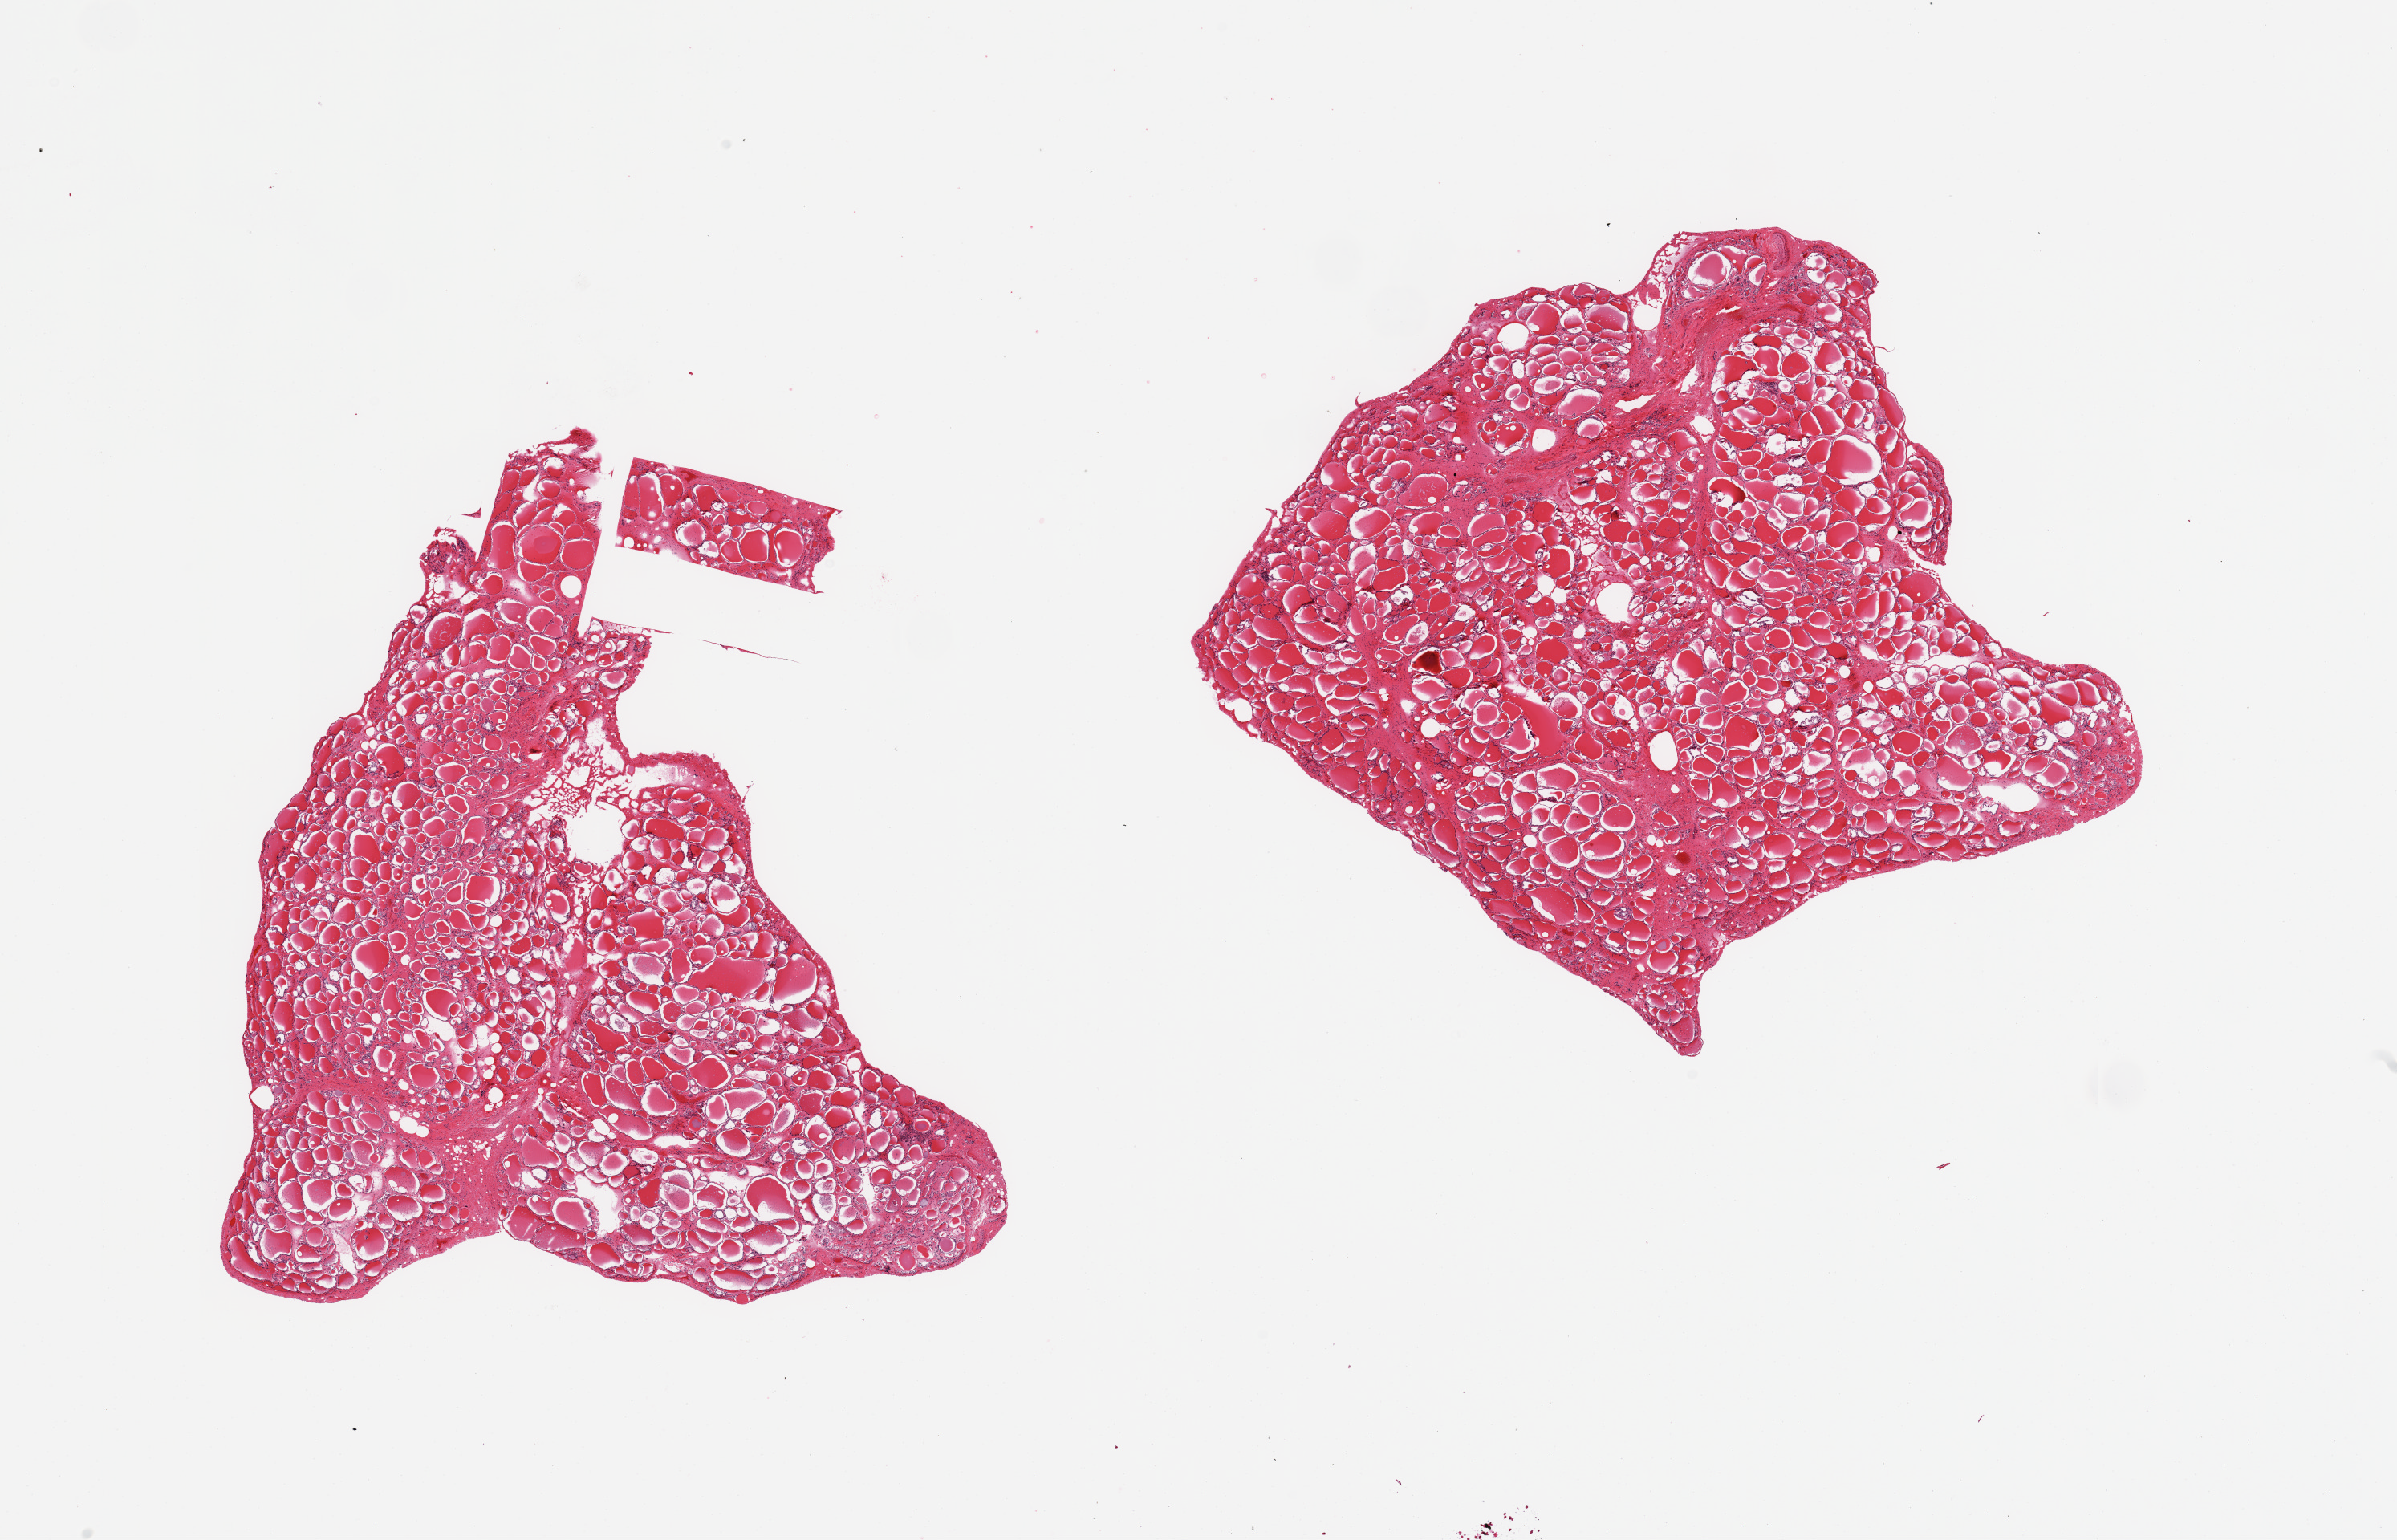
Digitized haematoxylin and eosin-stained section, brightfield — a low-resolution overview of the entire scanned area, about 23.6 x 15.2 mm; PAXgene-fixed paraffin-embedded (PFPE) section; sampled site (target tissue): thyroid; donor tissue sample. Donor: male.
Reviewer comment on this tissue sample: 2 pieces; well dissected.